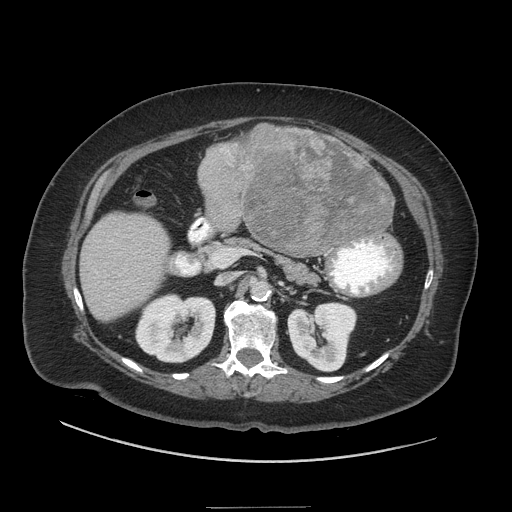
Contrast-enhanced abdominal CT (liver protocol), one axial slice; slice 12 of 81 in the series (ordered by position); reconstruction kernel STANDARD; 140 kVp; soft-tissue window (W 400 / L 40 HU); 2.5 mm slice thickness; 512 × 512 image matrix. Case-level facts recorded for this patient, not image findings: diagnosis: hepatocellular carcinoma (patient treated with transarterial chemoembolisation; whether this scan precedes or follows treatment is not stated here); TNM stage (as recorded): Stage-II; Child-Pugh class: A; tumour differentiation: moderately differentiated; tumour size: 1.7 cm.
Annotated regions visible in this slice (semi-automatic segmentation, software-assisted and operator-edited):
- liver parenchyma outside the tumour (the mass and vessels are separate outlines, so this box may not span the whole liver): box from (x=80, y=128) to (x=392, y=320) px
- mass: (x=197, y=125)–(x=396, y=255)
- liver vessels: (x=95, y=240)–(x=128, y=286)